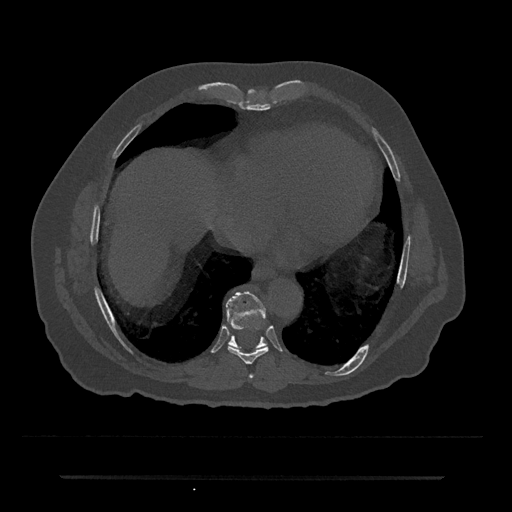
CT including the spine, one axial slice. Slice 312 of 797 in the series (ordered by position). Bone window (W 1800 / L 400 HU). 0.5 mm slice thickness. 512 × 512 image matrix. Male patient, age 69 years. Case-level facts recorded for this patient, not image findings: primary cancer: prostate.
Outlined on this slice (semi-automatically segmented with operator editing):
- T7 vertebra: bounding box <249,375,254,379> (left, top, right, bottom; pixels)
- T8 vertebra: <227,345,268,365>
- T9 vertebra: <226,291,267,347>